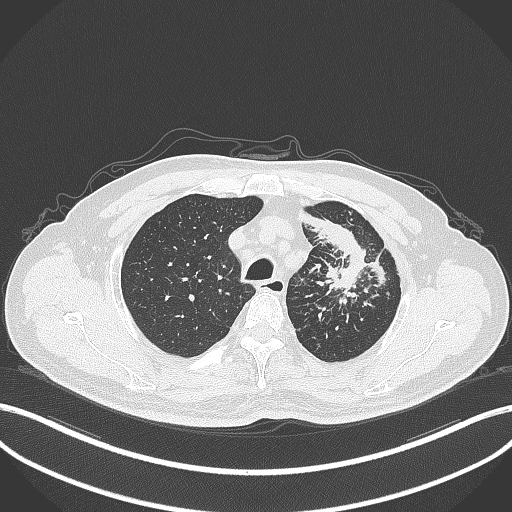
Chest CT, one axial slice. Position 286 of 386 along the scan axis. Reconstruction kernel B70f. Lung window (W 1500 / L -600 HU). 1 mm slice thickness. 512 × 512 image matrix. Male patient, age 69 years. Case-level facts recorded for this patient, not image findings: clinical TNM (as recorded): T2a N2 M0.
Structures marked on this image (rectangle marked by the reading radiologist):
- lung tumour (recorded histology: adenocarcinoma): box from (x=300, y=205) to (x=394, y=293) px